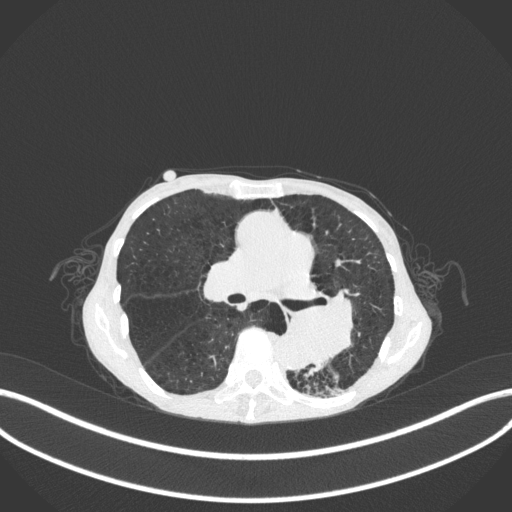
Chest CT, one axial slice. Position 158 of 347 along the scan axis. Reconstruction kernel B31f. Lung window (W 1500 / L -600 HU). 1 mm slice thickness. 512 × 512 image matrix, field of view 400 × 400 mm. Patient: female, 70 years. From the clinical record (not read from this slice): clinical TNM (as recorded): T3 N0 M0; histopathological grade: G3.
Annotated regions visible in this slice (rectangle marked by the reading radiologist):
- lung tumour (recorded histology: small cell carcinoma): bounding box (x1, y1, x2, y2) in pixels: (282, 286, 362, 373)